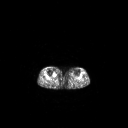
FDG PET of an extremity soft-tissue mass (from a PET/CT study), one axial slice. Slice 157 of 267 in the series (ordered by position). 3.27 mm slice thickness. 128 × 128 image matrix, field of view 700 × 700 mm. Female patient, age 65 years. Case-level facts recorded for this patient, not image findings: histological type: undifferentiated – high grade; grade: high; site of the primary tumour: right thigh.
Structures marked on this image (expert contour drawn on MRI and transferred to this co-registered scan by the dataset authors):
- gross tumour volume (mass): bounding box (x1, y1, x2, y2) in pixels: (53, 72, 56, 77)